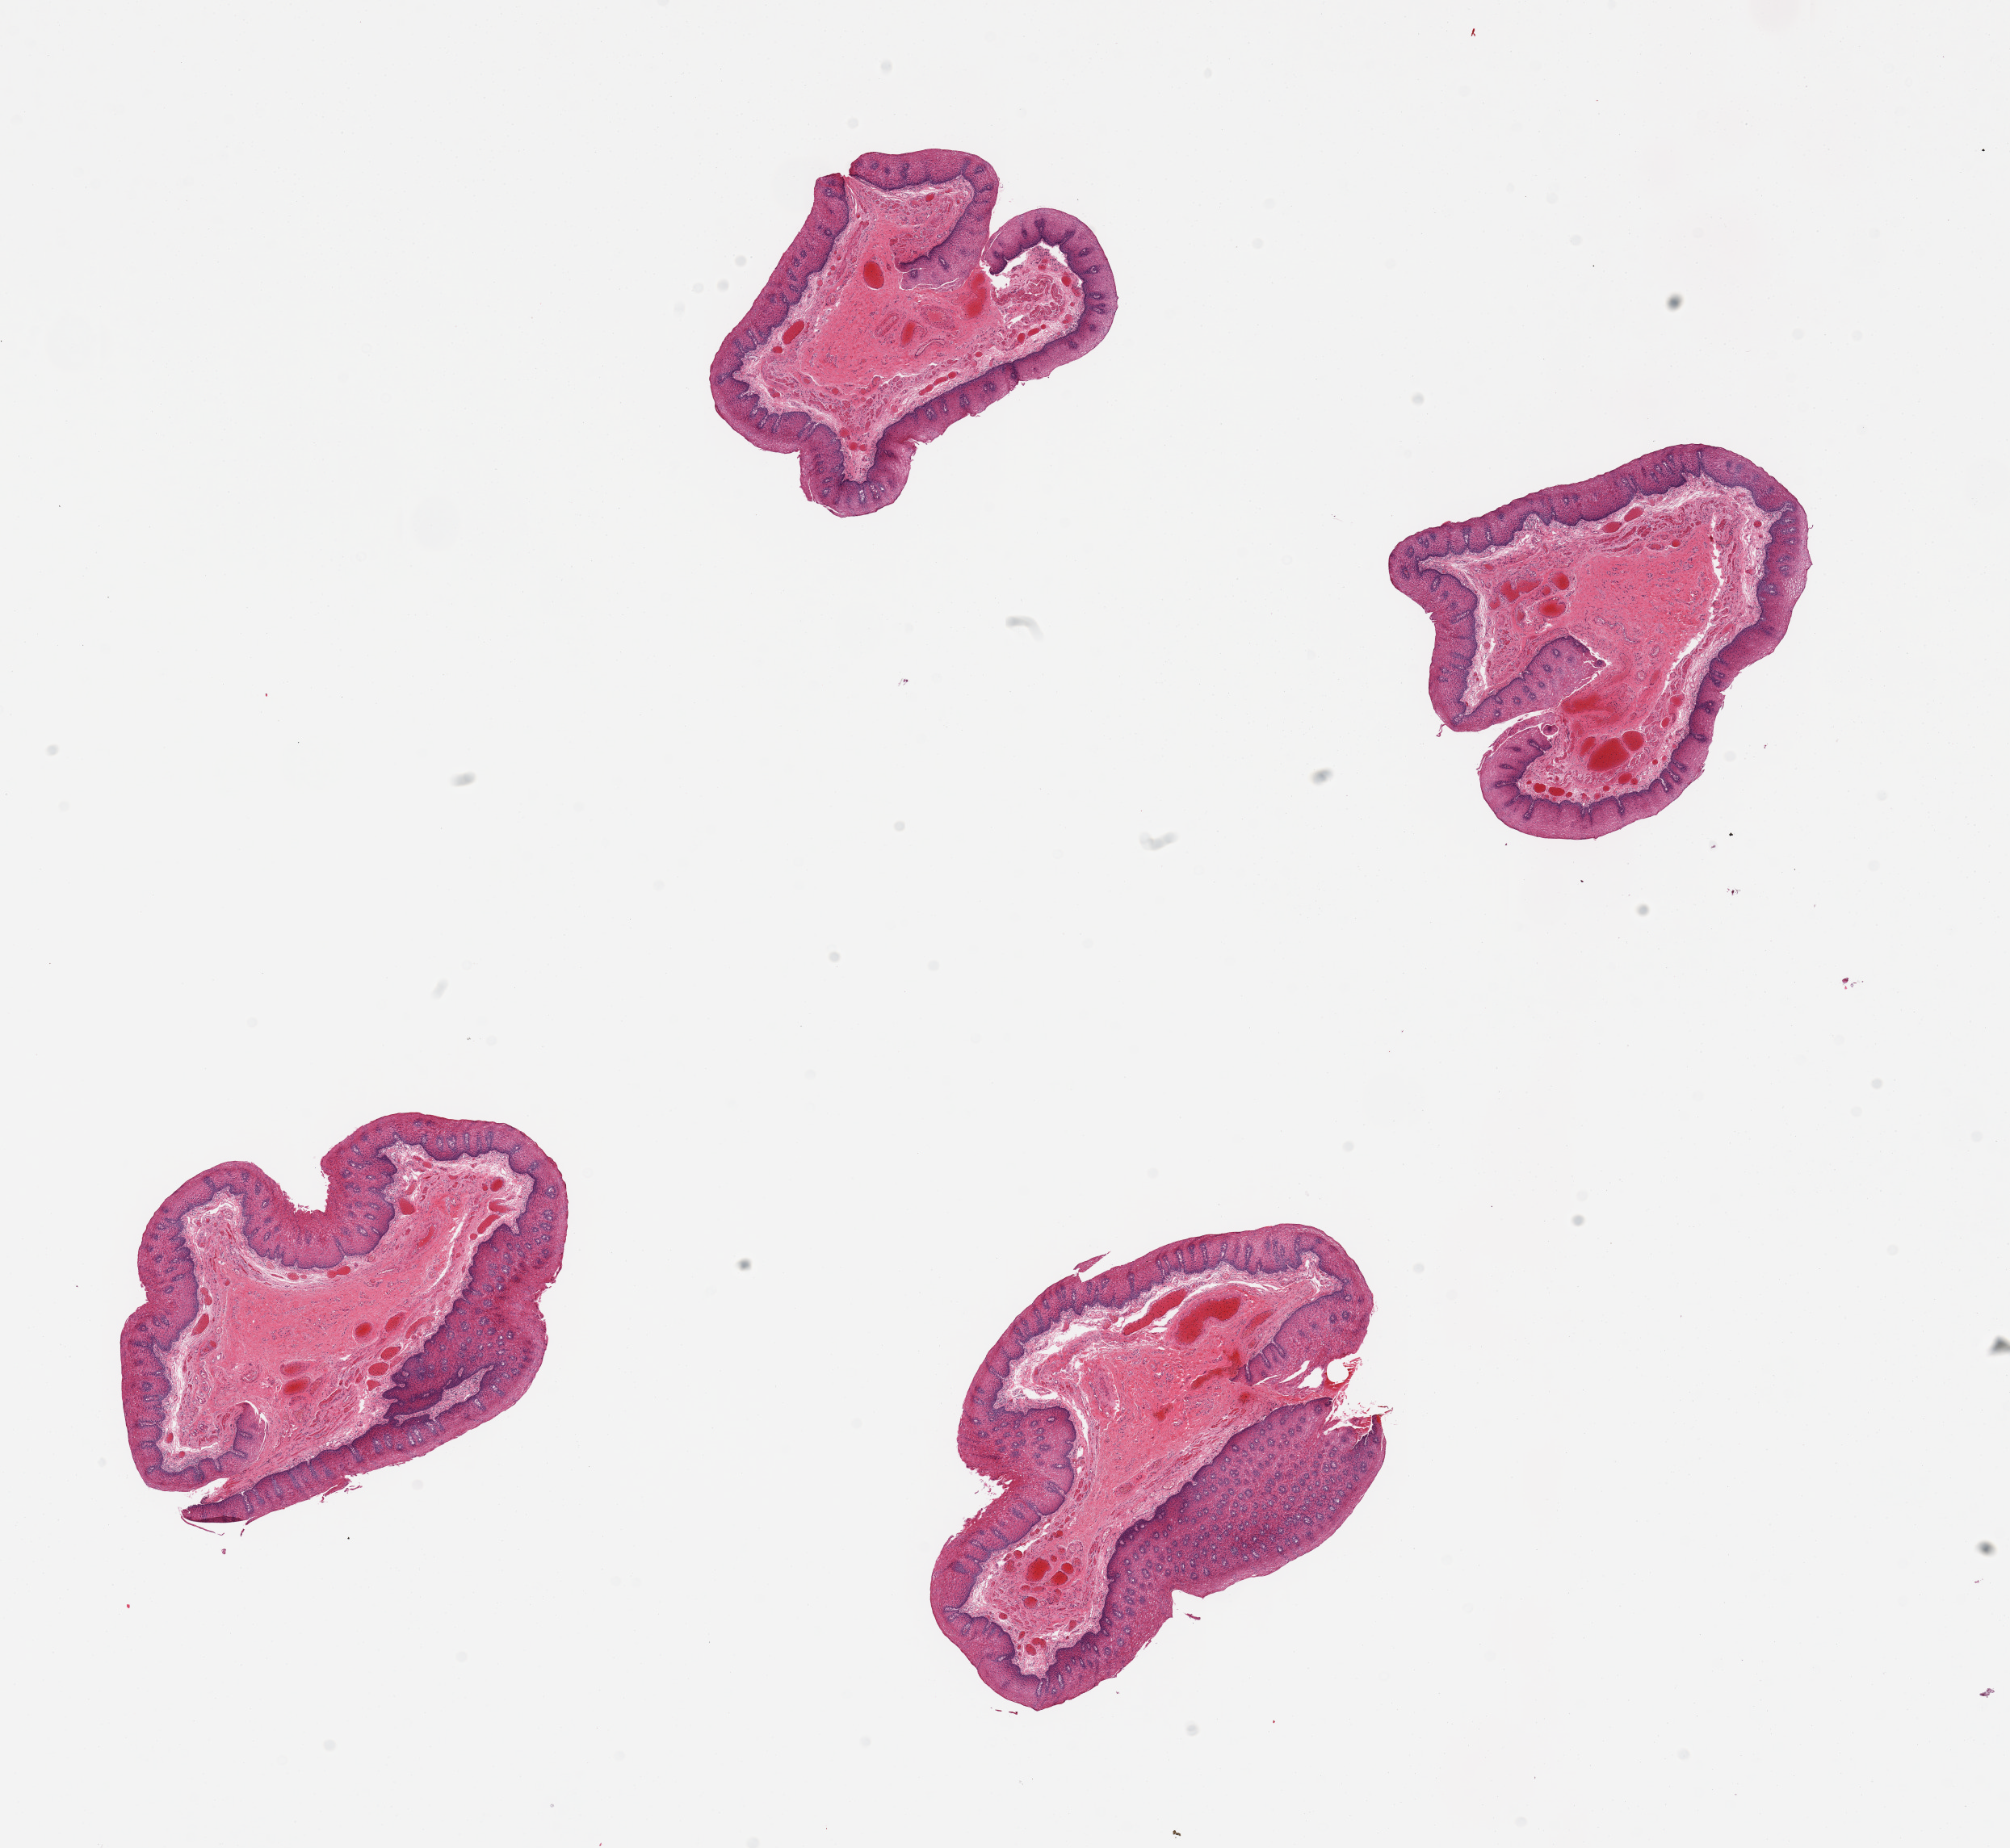
Digitized haematoxylin and eosin-stained section, low-resolution overview of the scanned area, about 19.7 x 18.1 mm; PAXgene-fixed paraffin-embedded (PFPE) section; sampled site (target tissue): esophageal mucous membrane; tissue donor sample. Male donor.
• reviewer comment on this tissue sample: 4 pieces, congested